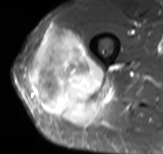
MRI of an extremity soft-tissue mass, one axial slice. Slice 44 of 61 in the series (ordered by position). STIR. MR volume resampled by the dataset authors to the PET/CT grid (not the native acquisition matrix). 163 × 154 image matrix, field of view 159 × 150 mm. Male patient. From the clinical record (not read from this slice): histological type: poorly differentiated synovial sarcoma; grade: high; site of the primary tumour: right buttock.
Annotated regions visible in this slice (expert contour drawn on MRI and transferred to this co-registered scan by the dataset authors):
- gross tumour volume including surrounding oedema: bounding box [x1, y1, x2, y2] px = [29, 25, 115, 124]
- gross tumour volume (mass): [29, 27, 111, 124]